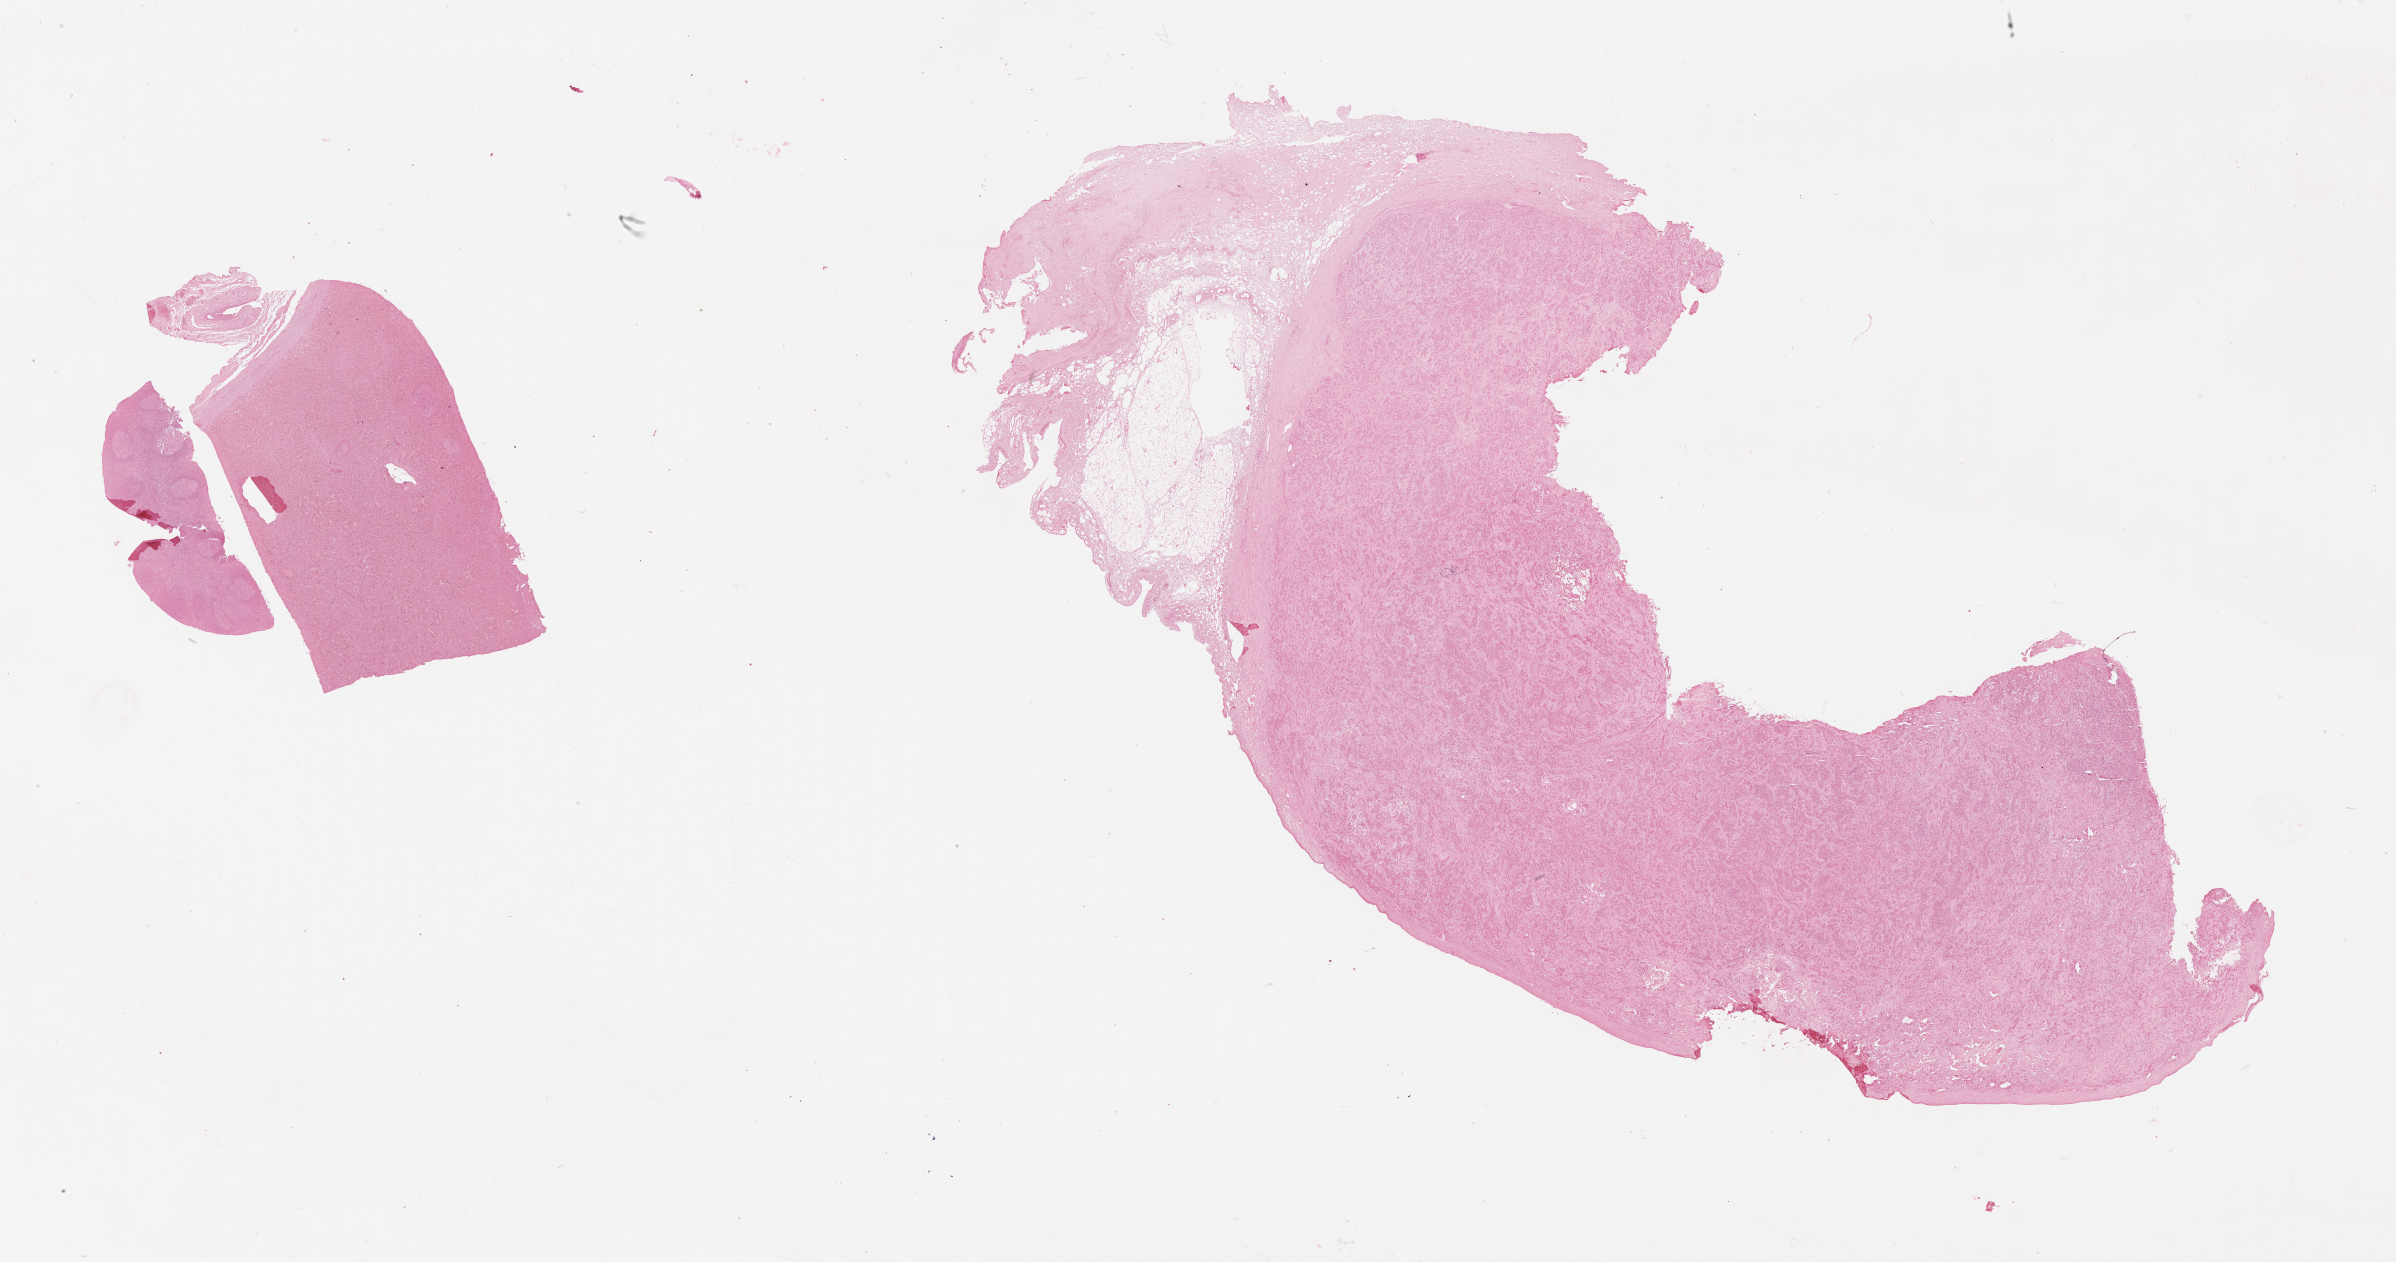
Whole-slide image, Epstein–Barr virus-encoded RNA (EBER) in-situ hybridisation, whole scanned area (about 38.7 x 20.4 mm) shown as a low-resolution overview, tumor tissue, site: bone. Patient male; 48 years old.
Diagnosis: Diffuse large B-cell lymphoma, NOS.